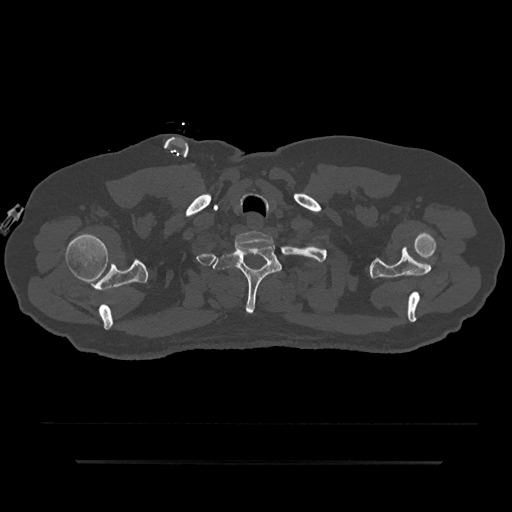
CT including the spine, one axial slice; position 740 of 797 along the scan axis; reconstruction kernel Br40s/3; 120 kVp; bone window (W 1800 / L 400 HU); 512 × 512 image matrix, field of view 464 × 464 mm. Male patient, age 59 years. From the clinical record (not read from this slice): primary cancer: bile ducts.
Annotated regions visible in this slice (semi-automatically segmented with operator editing):
- T1 vertebra: box from (x=213, y=245) to (x=282, y=313) px
- T2 vertebra: (x=288, y=283)–(x=292, y=285)